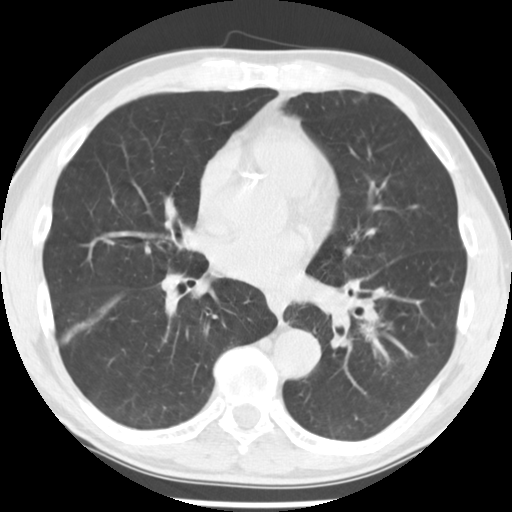
Axial slice from a low-dose chest CT screening exam; third screening round (two years after baseline); lung window (W 1500 / L -600 HU); 2.5 mm slice thickness; slice 111 of 242 in the series. Male, age 64 years at enrolment. Current smoker at enrolment.
Lesion marked by an expert reader, bounding box (x1, y1, x2, y2) in pixels: (352, 319, 389, 348). Screening reader's record for this exam: no non-calcified nodule ≥4 mm recorded.